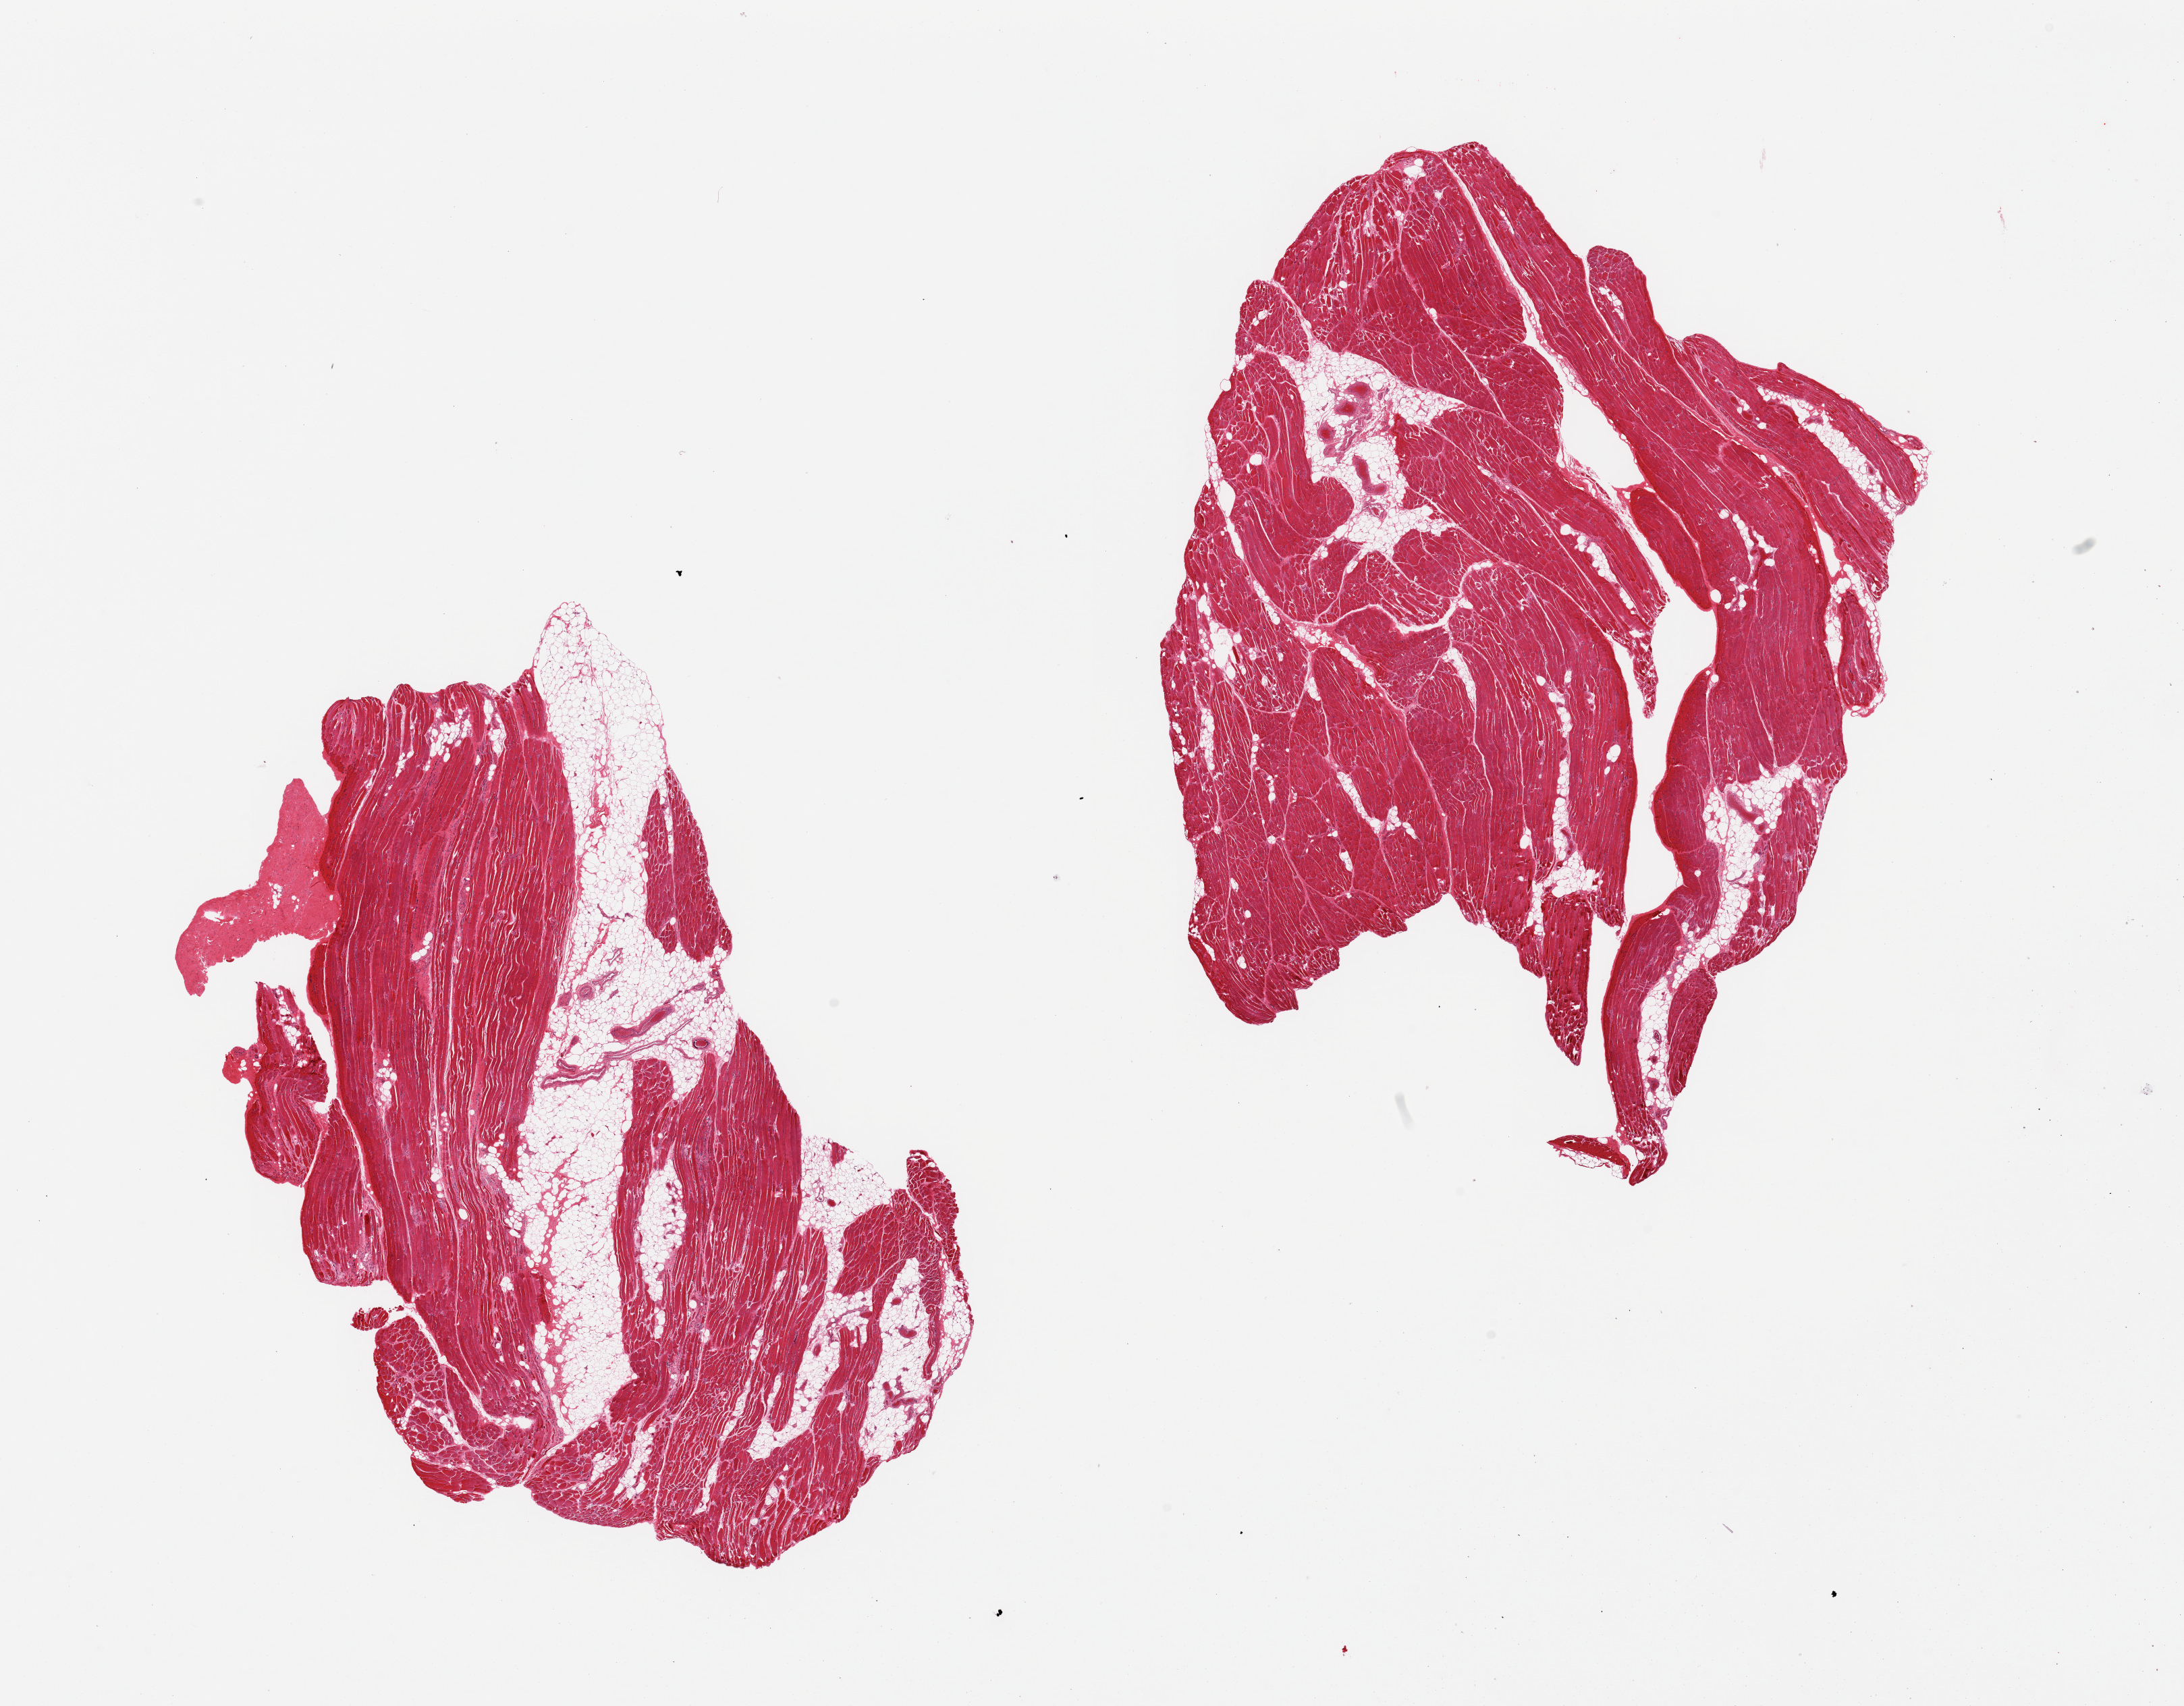
Whole-slide image, haematoxylin and eosin stain — whole scanned area (about 25.6 x 20.0 mm) shown as a low-resolution overview, PAXgene-fixed, paraffin-embedded tissue, target tissue: skeletal muscle, tissue donor sample. Donor: female.
Review note (as recorded): 2 pieces, 10-30% adipose tissue (predominantly internal), attached portion of tendon.